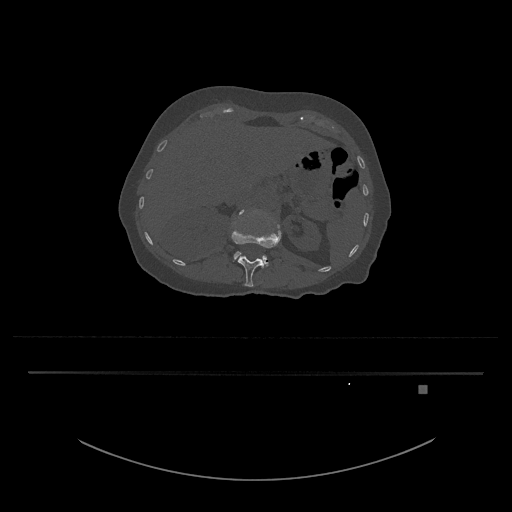
CT including the spine, one axial slice. Reconstruction kernel Br40s/3. 120 kVp. Bone window (W 1800 / L 400 HU). 0.5 mm slice thickness. 512 × 512 image matrix. Female patient, age 57 years. From the clinical record (not read from this slice): primary cancer: cervical.
Outlined on this slice (semi-automatically segmented with operator editing):
- L1 vertebra: bounding box (x1, y1, x2, y2) in pixels: (232, 222, 282, 287)